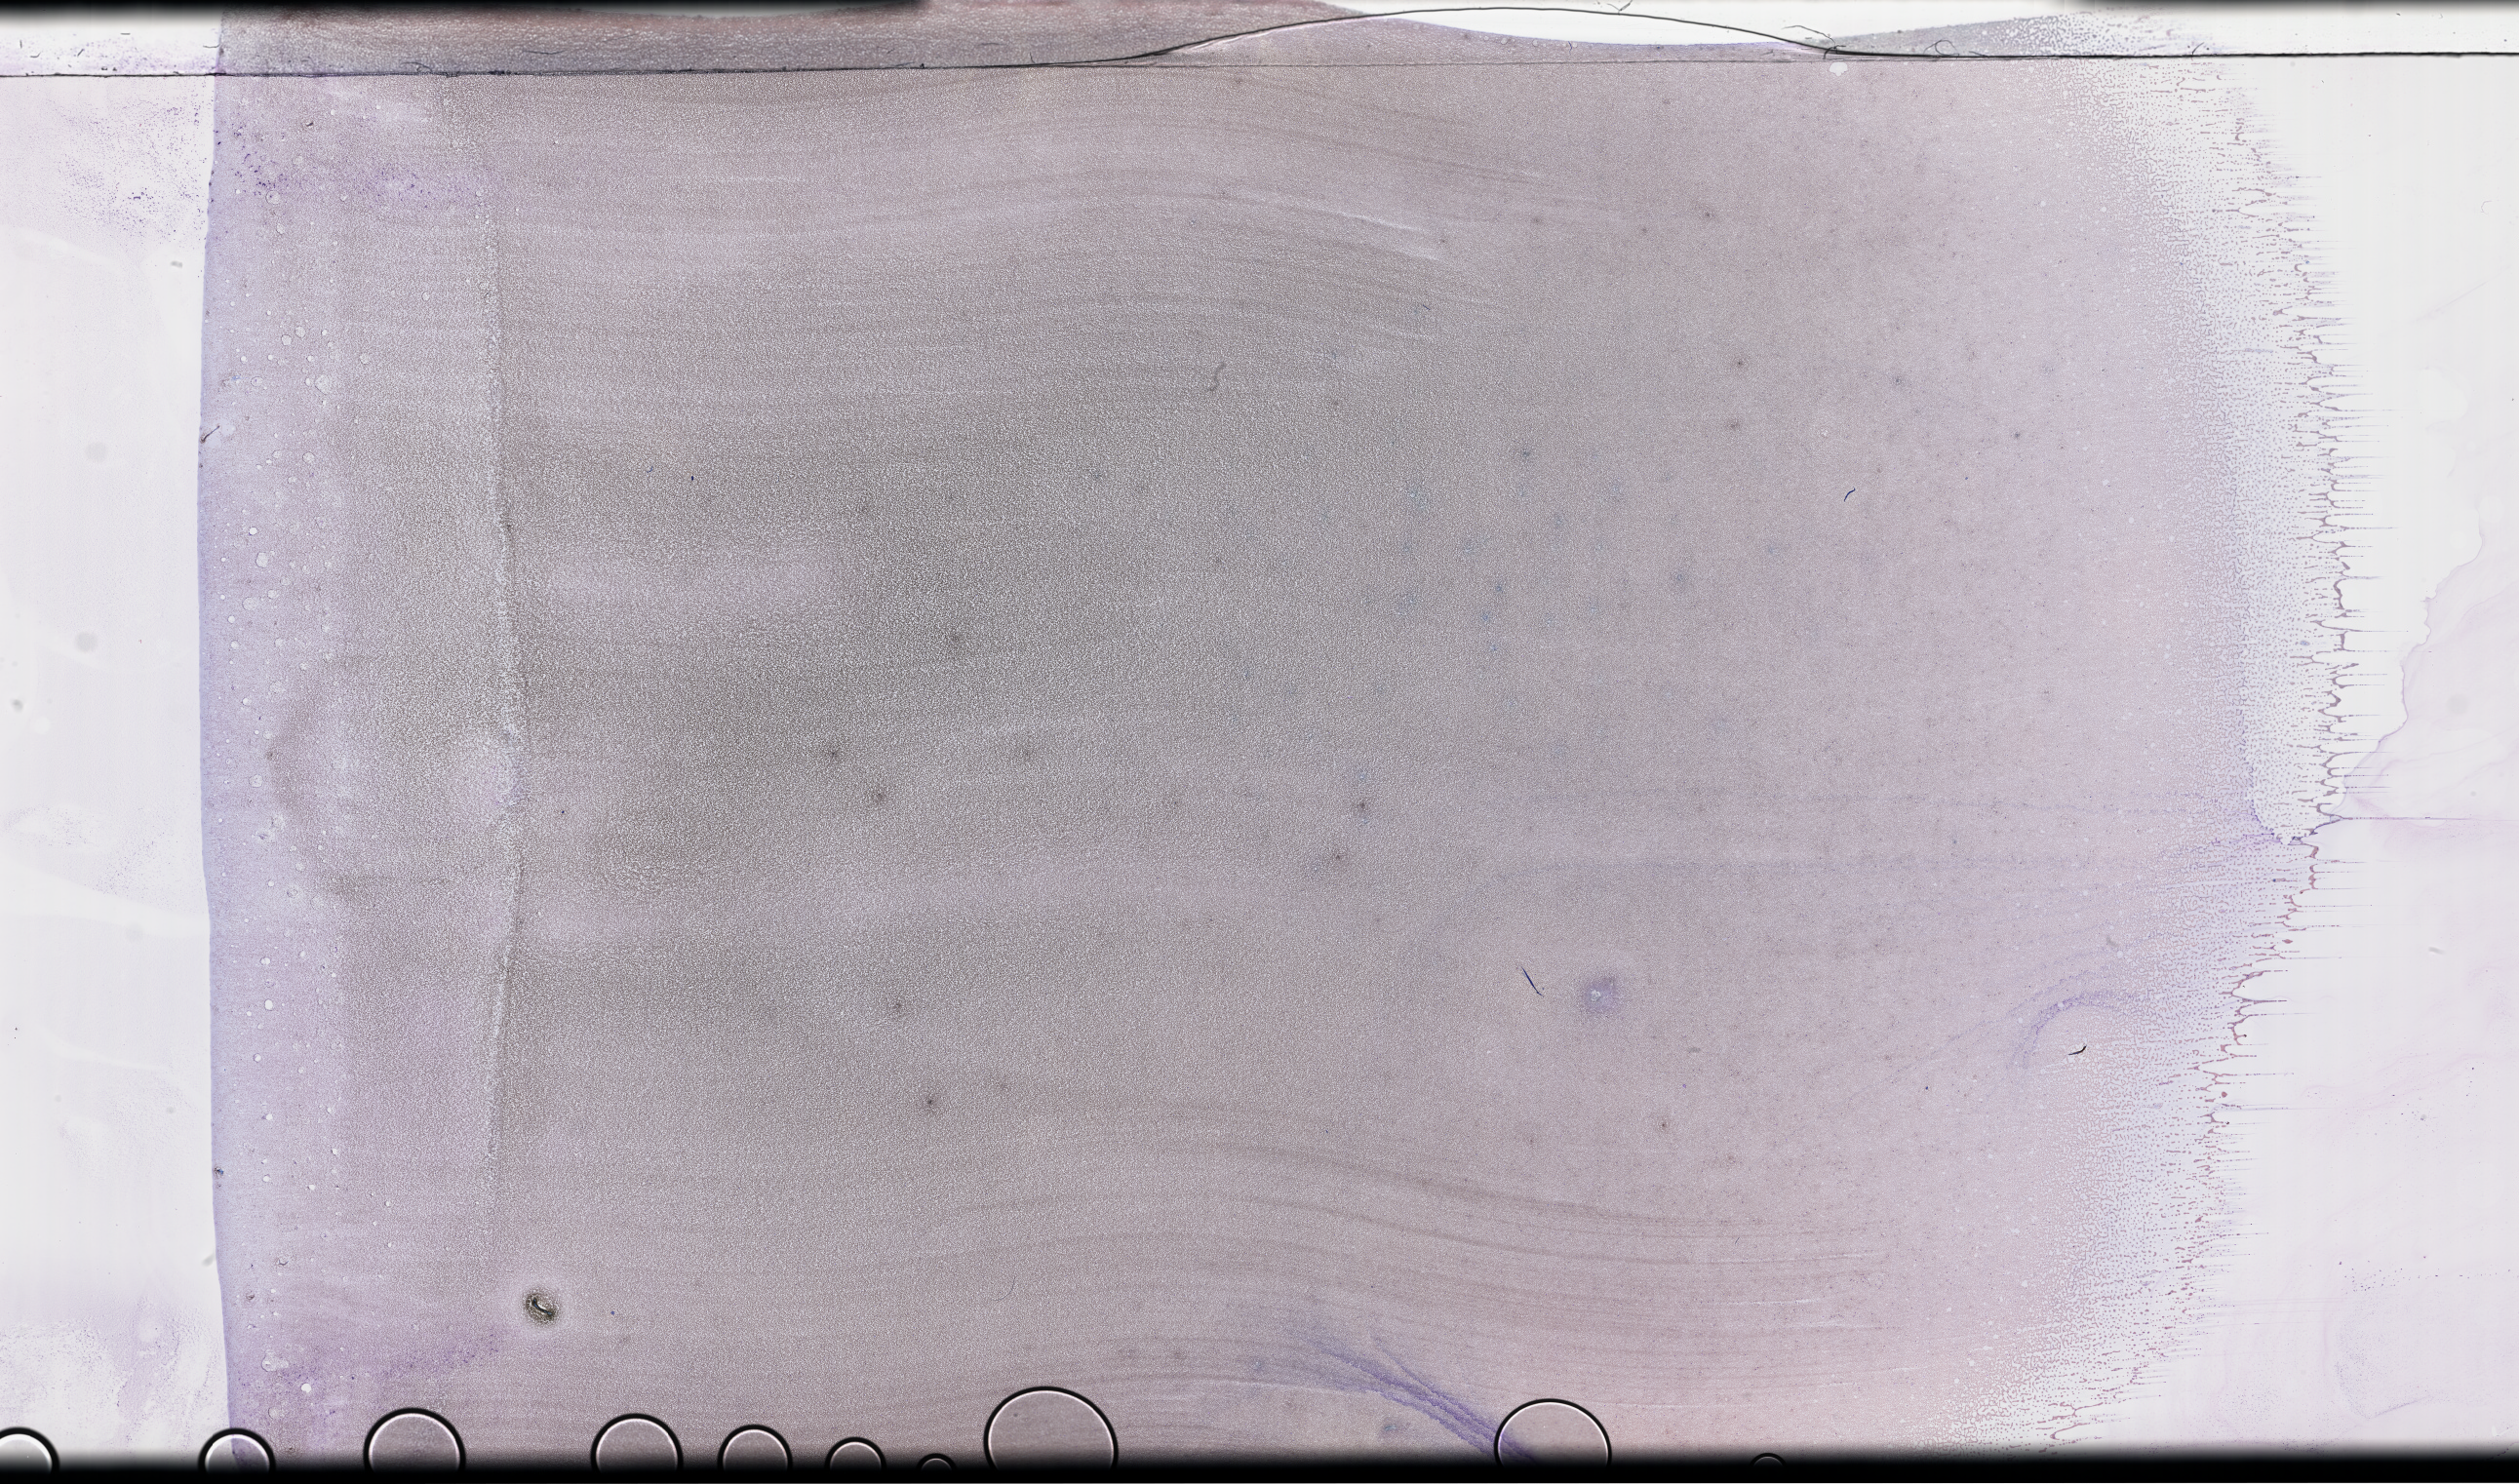
Wright-Giemsa-stained whole blood smear, whole-slide image — whole scanned area (about 41.7 x 24.6 mm) shown as a low-resolution overview. Patient: female.
From a patient with: Plasma Cell Myeloma.